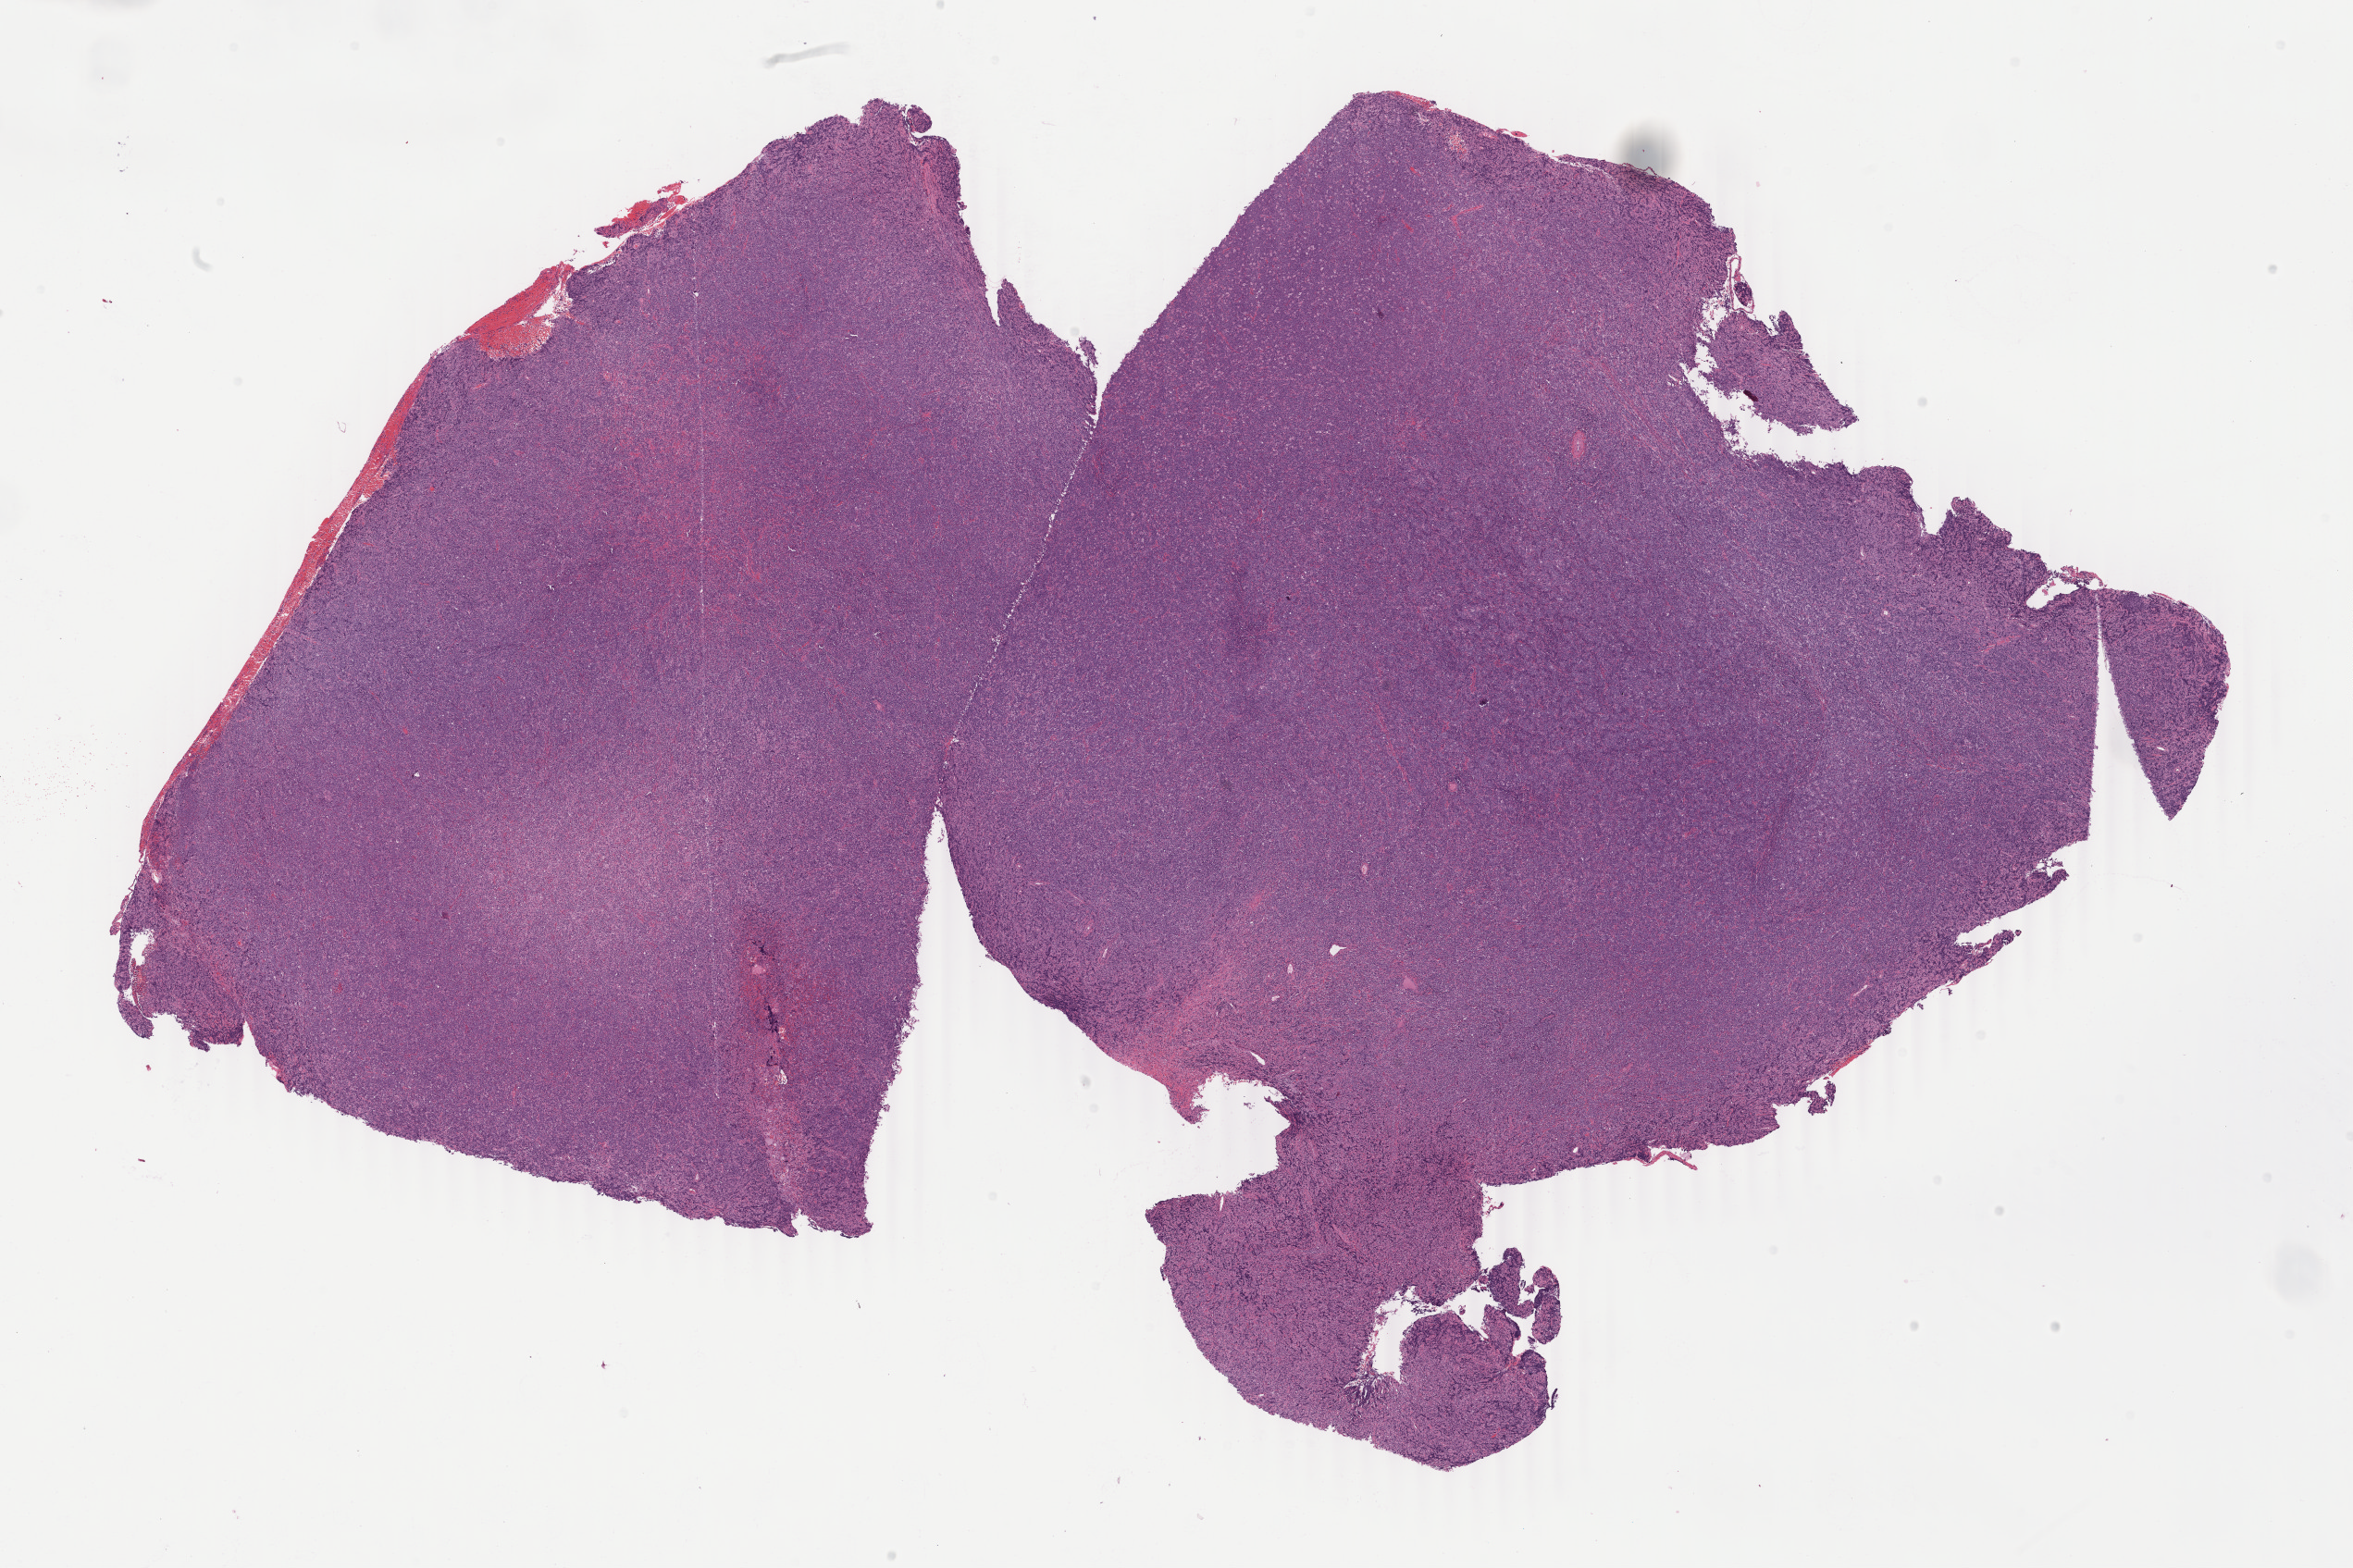
Whole-slide image, hematoxylin and eosin (H&E) stain, shown as a low-resolution overview of the whole scanned area (about 20.2 x 13.5 mm), tumor tissue. Patient: male, age at initial diagnosis 7 years.
Histologic diagnosis: Diffuse large B-cell lymphoma, NOS.